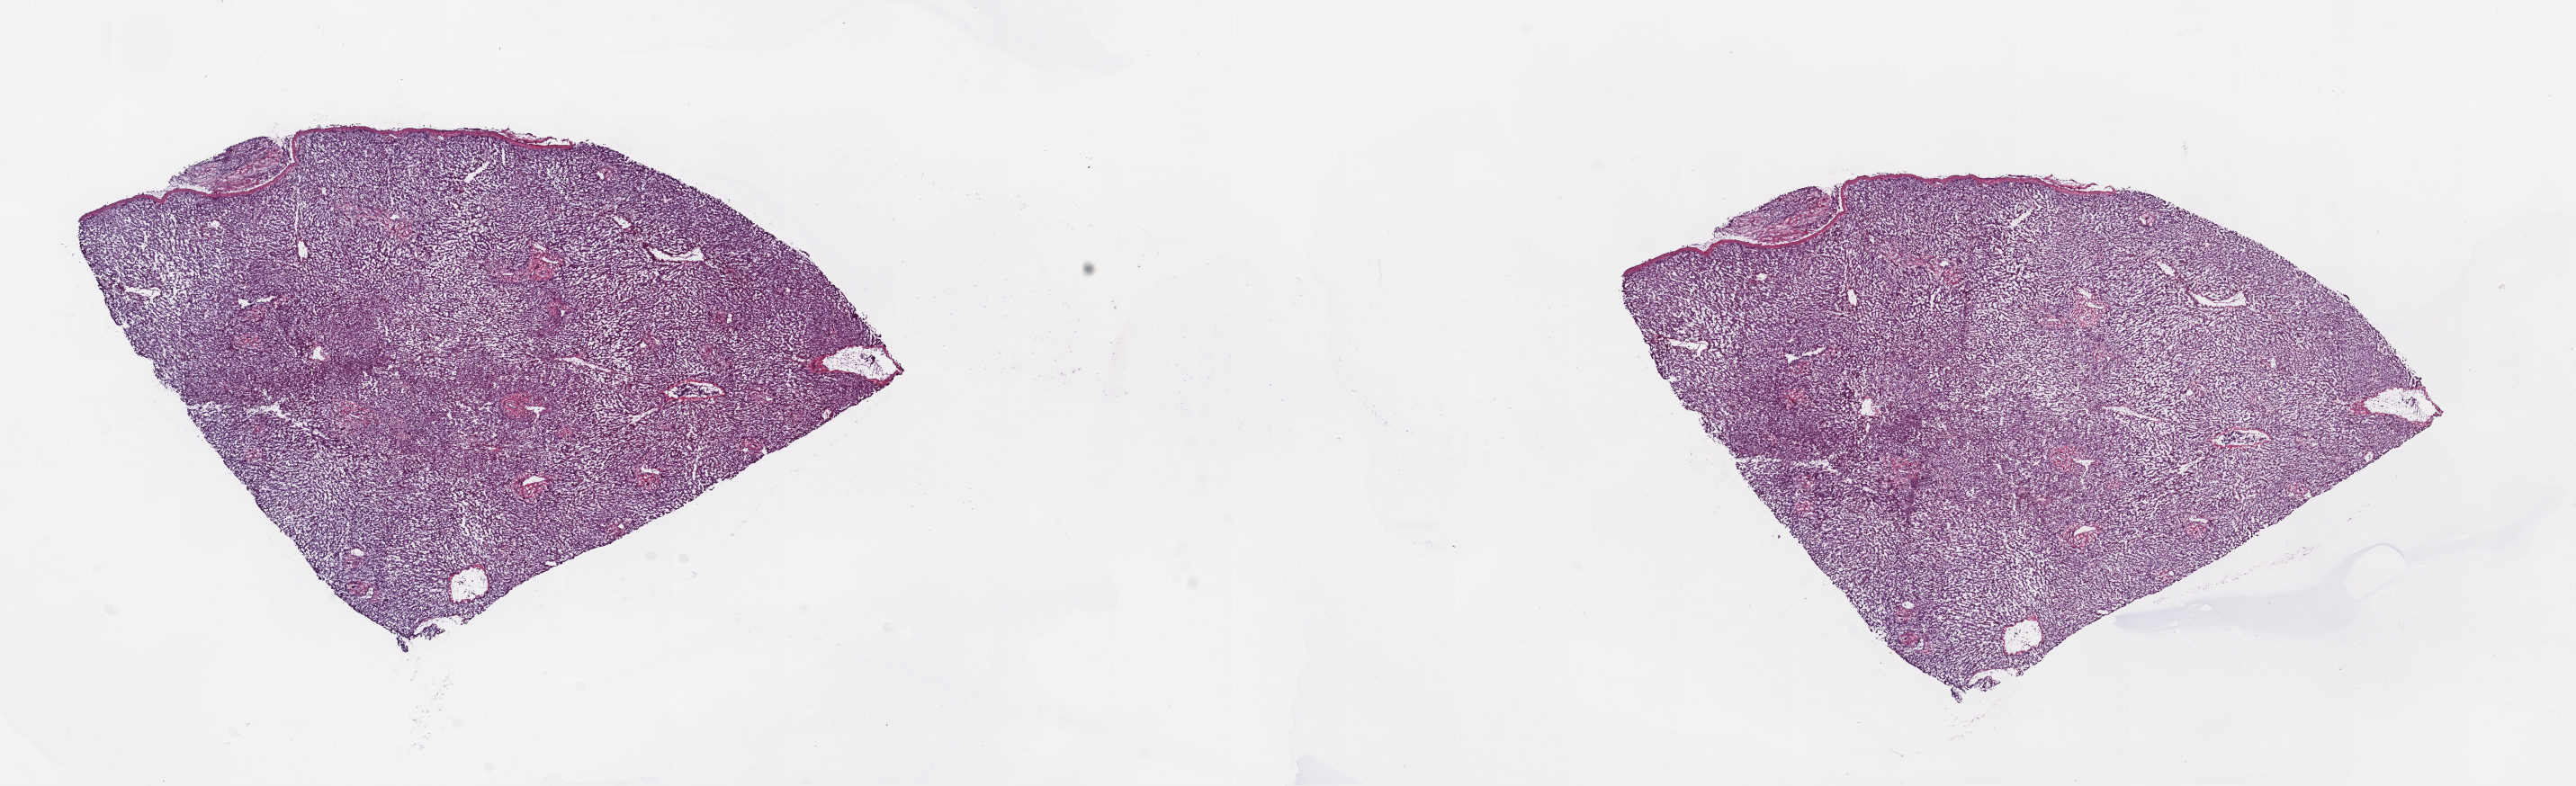
Digitized H&E-stained tissue section (whole slide) — shown as a low-resolution overview of the whole scanned area (about 22.6 x 6.9 mm). Frozen section from the top of the tissue portion. Liver, solid tissue normal (non-tumour tissue) sample. Male, age 75 years at initial diagnosis. Slide review estimates, as recorded: tumour cells 0%, tumour nuclei 0%, normal cells 100%, stromal cells 0%, necrosis 0%. Inflammatory infiltration, as recorded: lymphocyte infiltration 0%, monocyte infiltration 0%, neutrophil infiltration 0%.
This section: solid tissue normal (non-tumour) sample from the same patient. Patient diagnosis: Hepatocellular carcinoma, NOS.